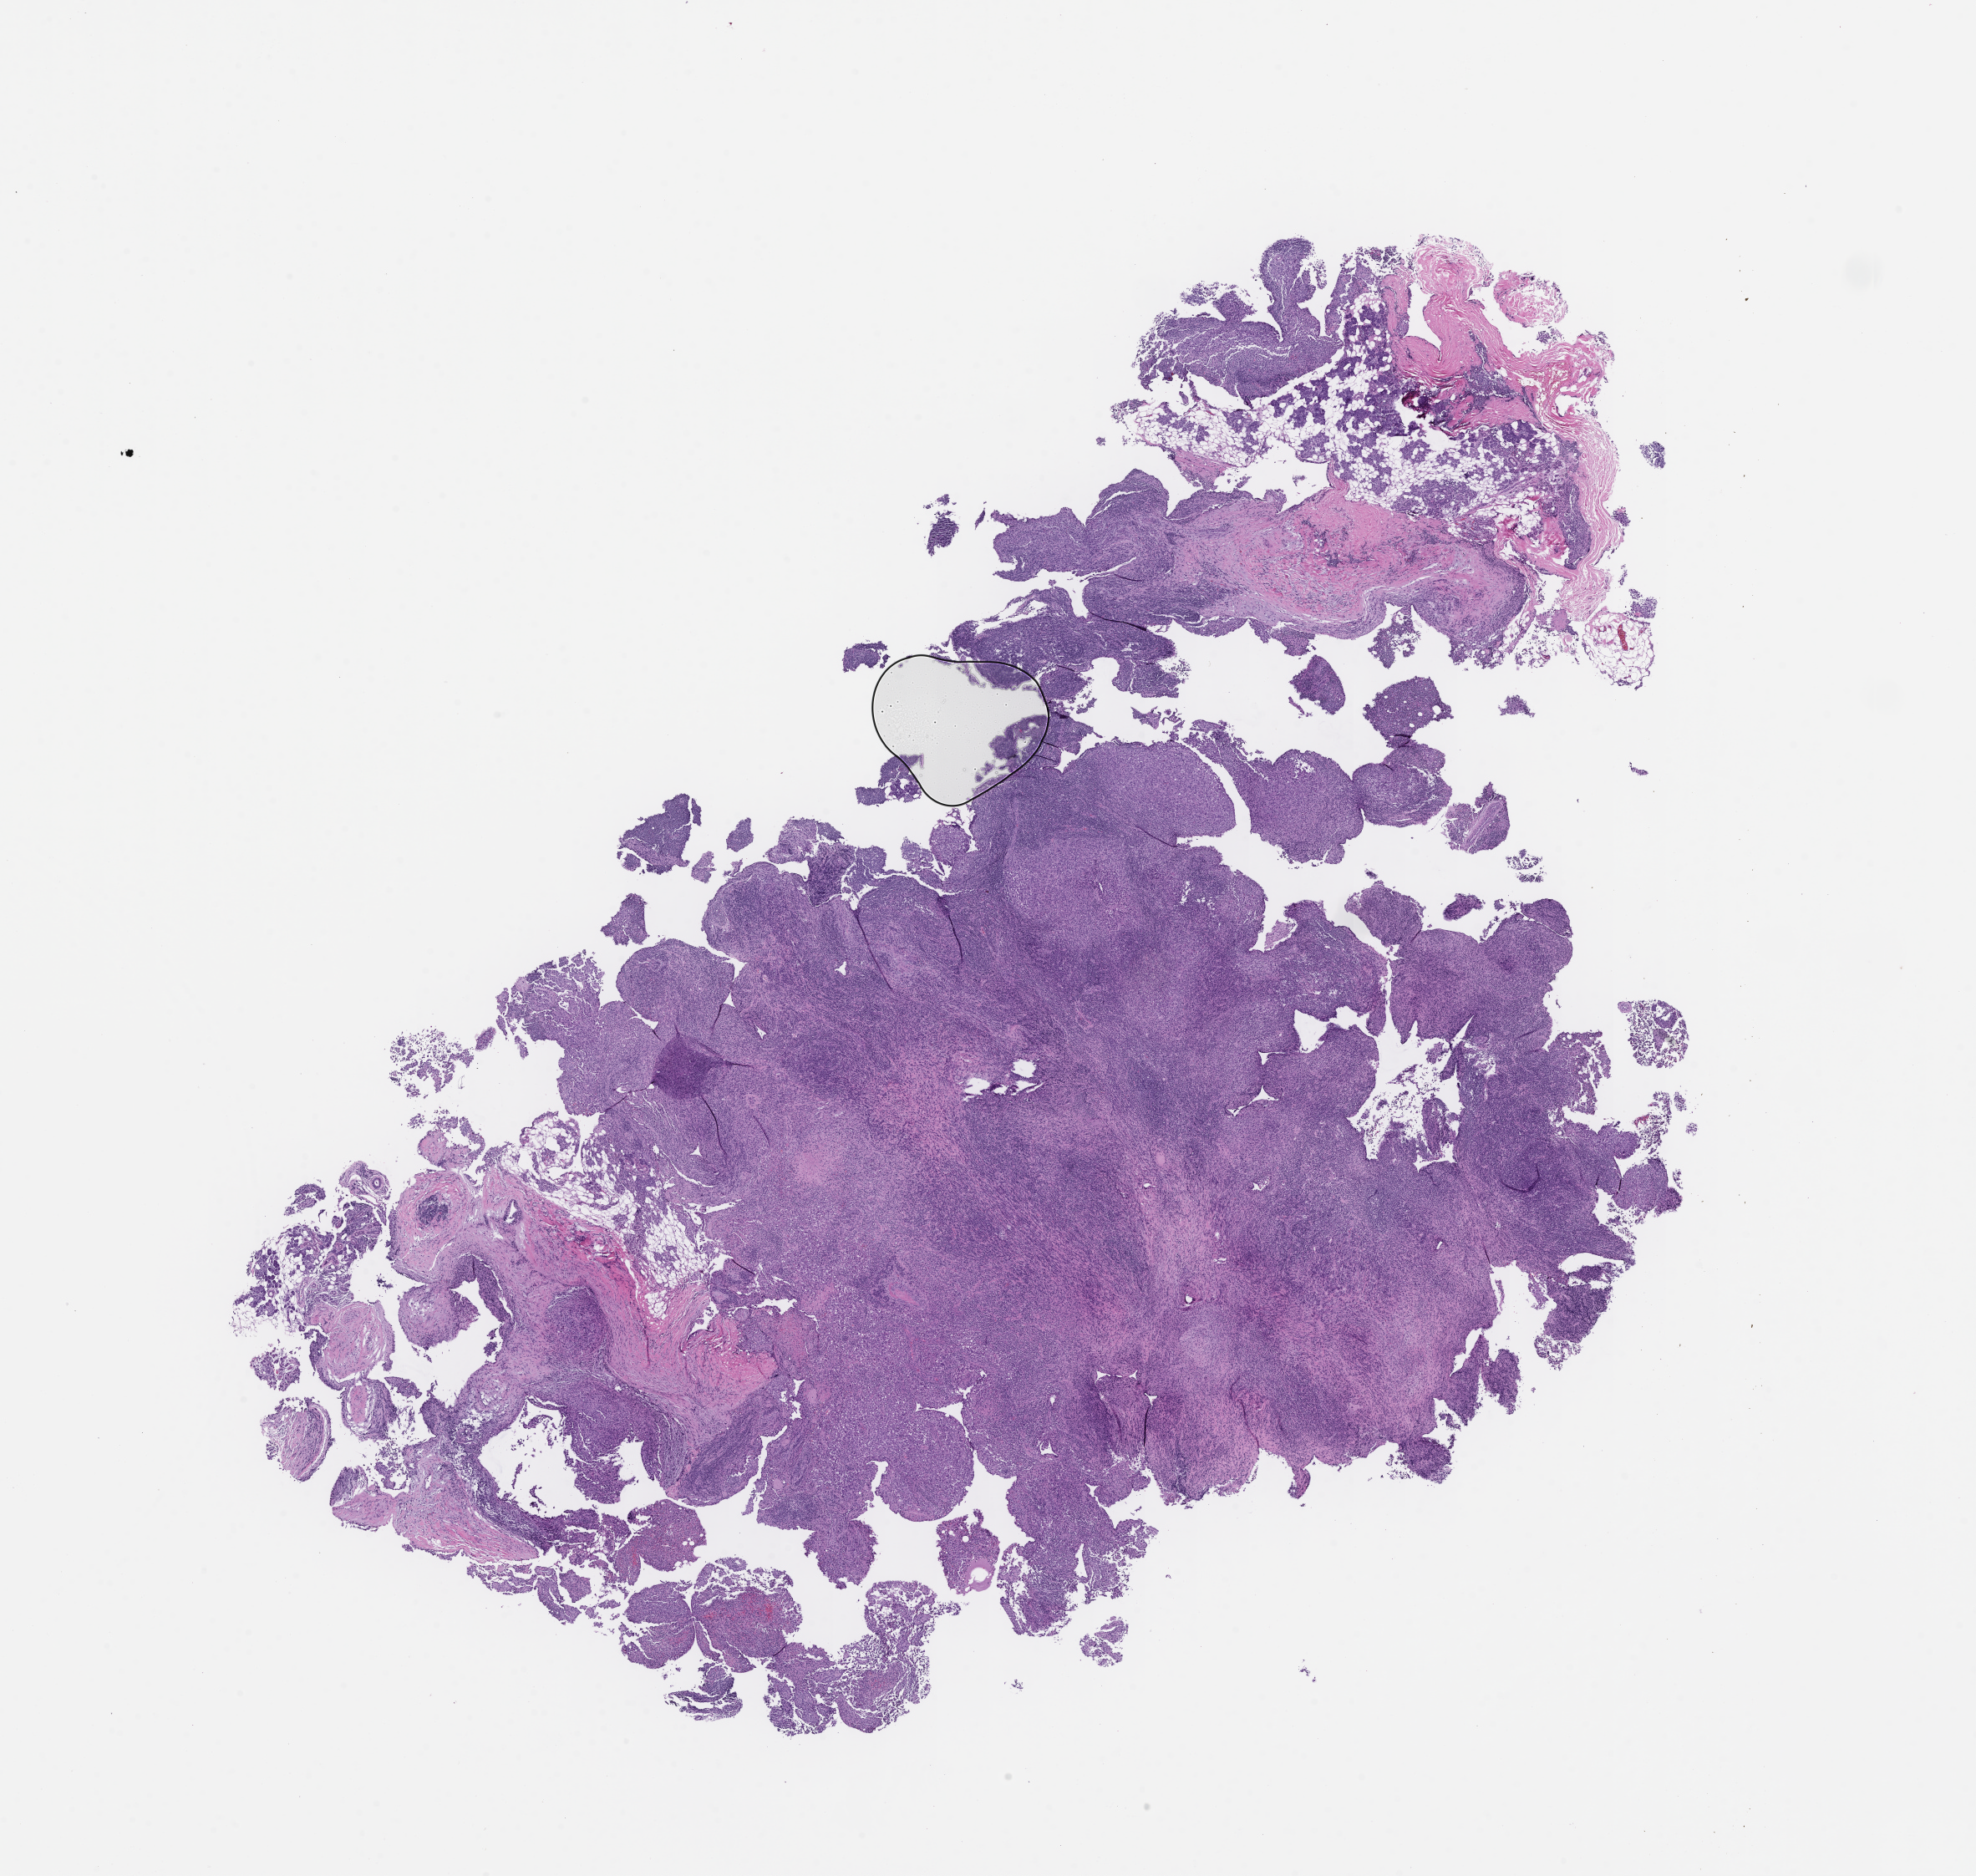
Haematoxylin and eosin whole-slide image, shown as a low-resolution overview of the whole scanned area (about 19.1 x 18.1 mm), formalin-fixed paraffin-embedded section, specimen time point: collected on treatment. Patient: male.
This section: metastasis (sampled organ not recorded). Primary diagnosis of the patient: Melanoma.